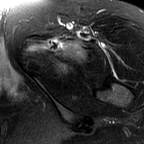
MRI of an extremity soft-tissue mass, one axial slice; position 50 of 60 along the scan axis; T2-weighted fat-saturated; MR volume resampled by the dataset authors to the PET/CT grid (not the native acquisition matrix); 3.27 mm slice thickness; 144 × 144 image matrix, field of view 141 × 141 mm. Female patient. From the clinical record (not read from this slice): histological type: pleiomorphic leiomyosarcoma; grade: intermediate; site of the primary tumour: left thigh.
Outlined on this slice (expert contour drawn on MRI and transferred to this co-registered scan by the dataset authors):
- gross tumour volume including surrounding oedema: box from (x=25, y=38) to (x=89, y=73) px
- gross tumour volume (mass): (x=61, y=42)–(x=83, y=59)